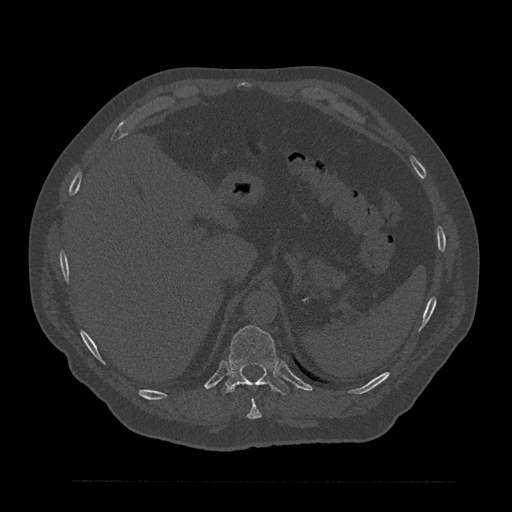
CT including the spine, one axial slice; slice 309 of 797 in the series (ordered by position); reconstruction kernel Br40s/3; 120 kVp; bone window (W 1800 / L 400 HU); 0.5 mm slice thickness; 512 × 512 image matrix. Male patient, age 61 years. Case-level facts recorded for this patient, not image findings: primary cancer: prostate.
Structures marked on this image (semi-automatically segmented with operator editing):
- T10 vertebra: bounding box <247,399,262,419> (left, top, right, bottom; pixels)
- T11 vertebra: <221,325,289,395>